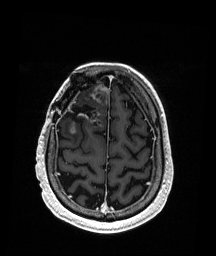
Brain MRI from a brain-tumour surgery series, one axial slice; slice 47 of 192 in the series (ordered by position); T1-weighted post-contrast; 1 mm slice thickness; 216 × 256 image matrix, field of view 211 × 250 mm. Case-level facts recorded for this patient, not image findings: histopathology: Astrocytoma; WHO grade: 3; IDH mutation: yes.
Outlined on this slice (expert manual segmentation):
- previous resection cavity: bounding box [x1, y1, x2, y2] px = [65, 93, 101, 126]
- tumour: [69, 85, 109, 134]